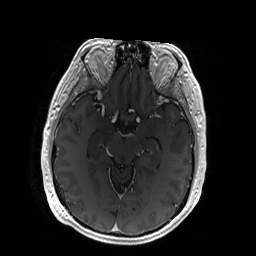
Brain MRI from a brain-tumour surgery series, one axial slice. Slice 112 of 192 in the series (ordered by position). T1-weighted post-contrast. 1 mm slice thickness. 256 × 256 image matrix, field of view 256 × 256 mm. From the clinical record (not read from this slice): histopathology: Glioblastoma; WHO grade: 4; IDH mutation: no.
Structures marked on this image (expert manual segmentation):
- tumour: box from (x=128, y=134) to (x=158, y=152) px